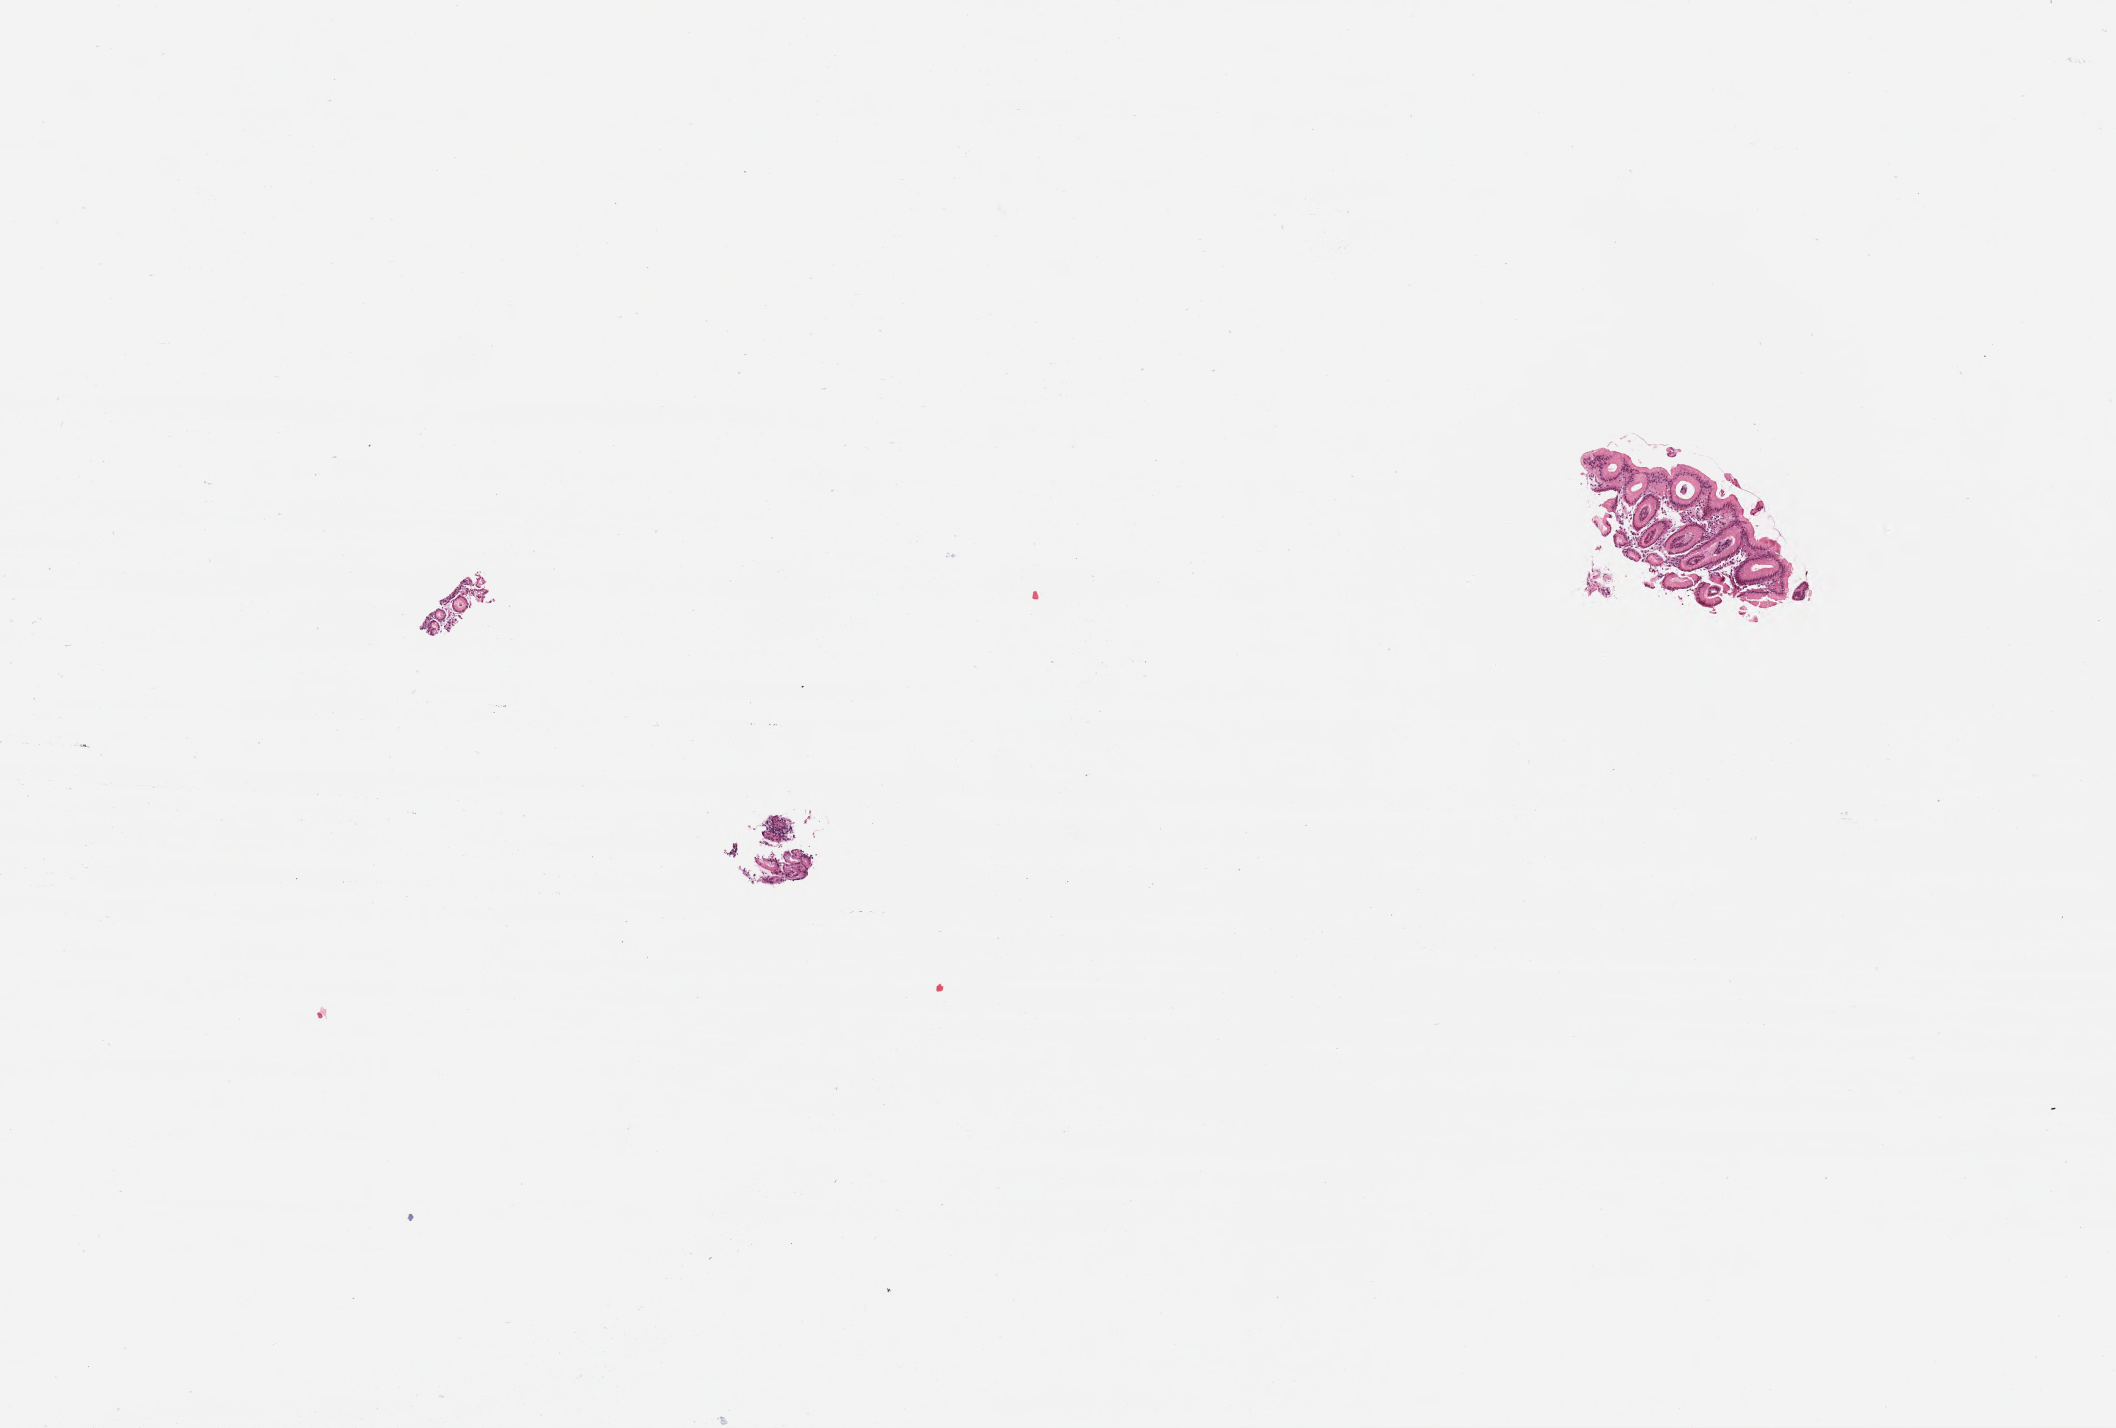
Digitized haematoxylin and eosin-stained section — shown as a low-resolution overview of the whole scanned area (about 8.6 x 5.8 mm); formalin-fixed, paraffin-embedded (FFPE) tissue; non-tumor (normal tissue) sample from a patient with burkitt lymphoma, NOS. Patient: male, age 36 years. Pathologist review of this section (percent, as recorded): tumor cells 0%, tumor nuclei 0%, stromal cells 0%, necrosis 0%, normal cells 100%. Inflammatory infiltration, as recorded: lymphocyte infiltration 20%, monocyte infiltration 20%, neutrophil infiltration 10%.
This section: non-tumor tissue sample; the patient's diagnosis is given above.